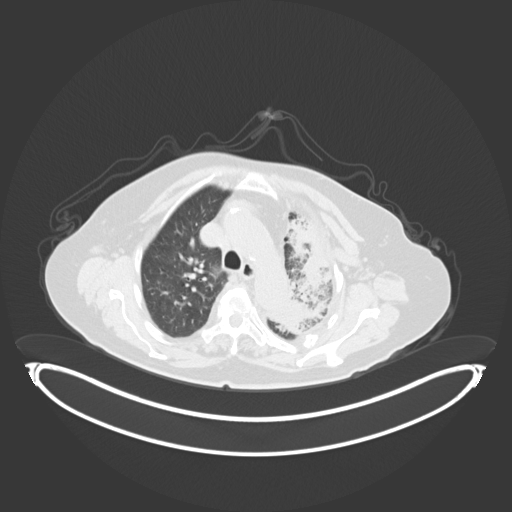
Chest CT, one axial slice. Slice 218 of 284 in the series (ordered by position). Reconstruction kernel B30f. Lung window (W 1500 / L -600 HU). 512 × 512 image matrix, field of view 500 × 500 mm. Female patient, age 75 years. Case-level facts recorded for this patient, not image findings: clinical TNM (as recorded): T3 N3 M1.
Structures marked on this image (bounding box drawn by a radiologist):
- lung tumour (recorded histology: adenocarcinoma): box from (x=270, y=210) to (x=335, y=335) px